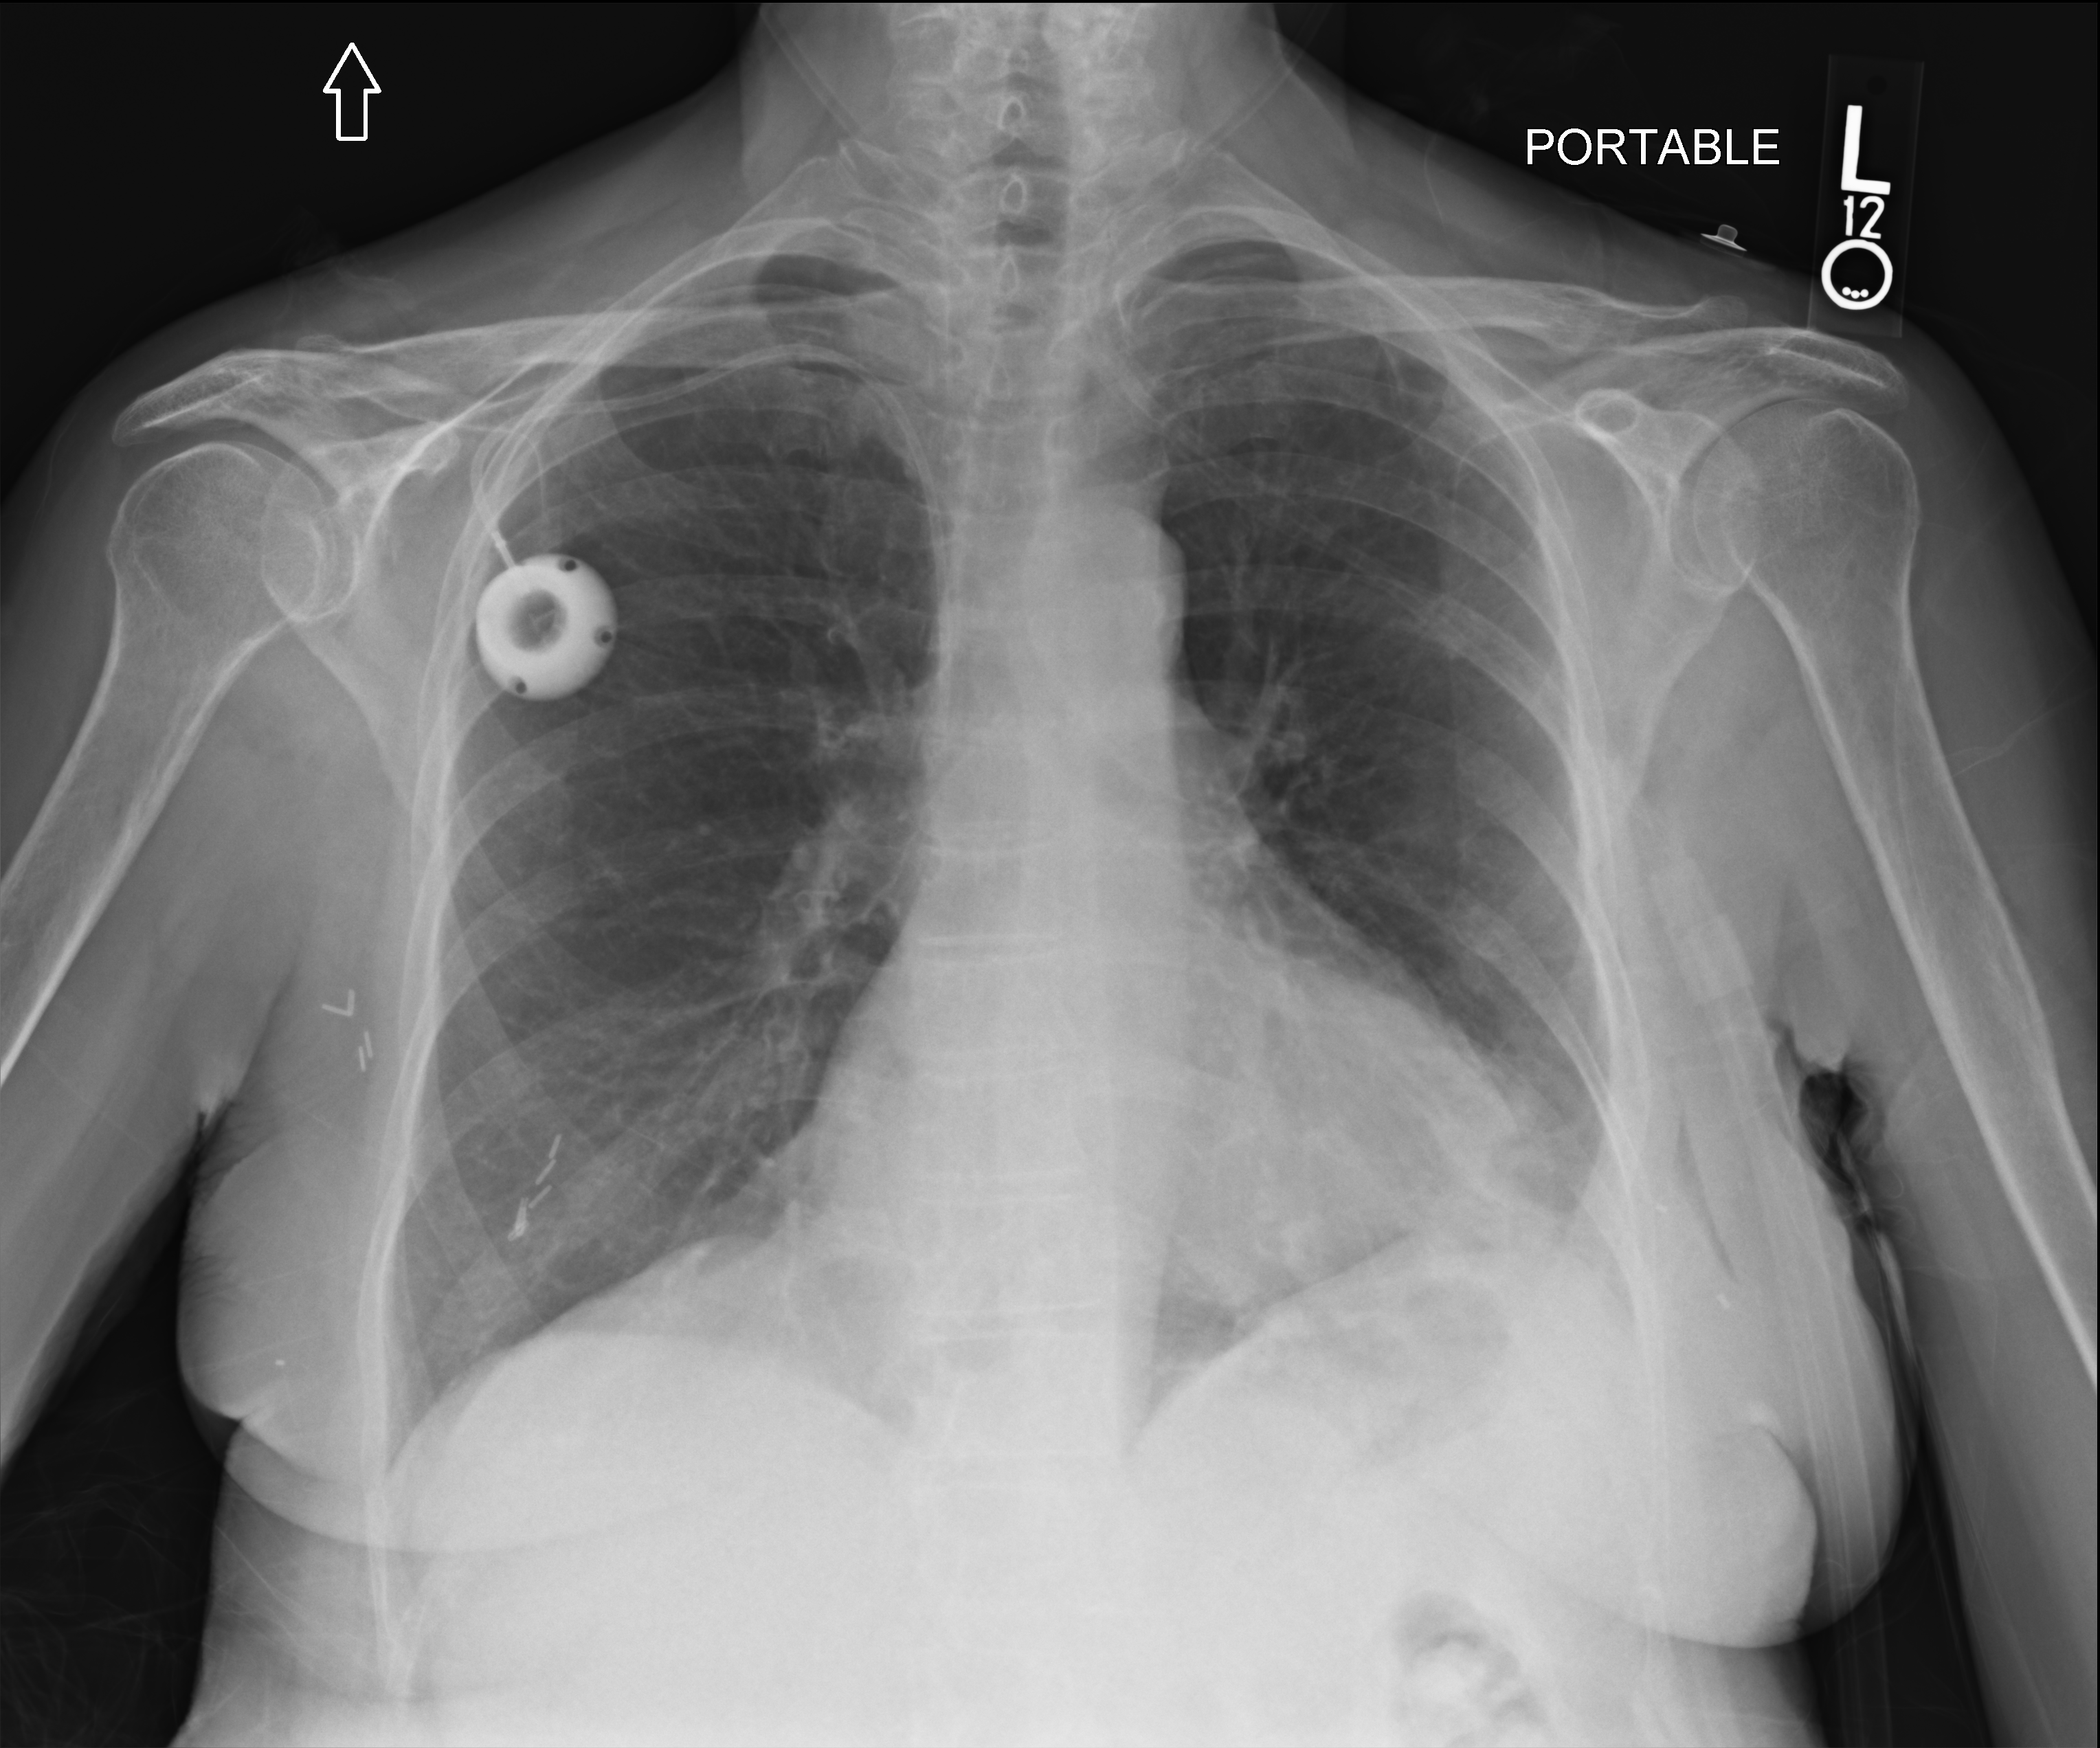
Chest X-ray (portable); anteroposterior (AP) projection. Patient hospitalised with COVID-19; female, aged 60–74 years.
From the hospital-stay record, not from the radiograph (when in the stay this image was taken is not recorded):
- mechanically ventilated during this hospital stay: yes
- hypertension (admission record): yes